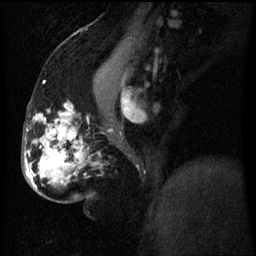
Breast MRI (dynamic contrast-enhanced), one sagittal slice; position 31 of 60 along the scan axis; dynamic contrast-enhanced series, image 2 of 3 at this slice position (ordered by acquisition); 1.5 T; TE 4.2 ms, TR 8 ms; 2.5 mm slice thickness; 256 × 256 image matrix, field of view 200 × 200 mm. Patient: female, 50 years.
Annotated regions visible in this slice (semi-automatically segmented with operator editing):
- analysis volume of interest (the breast-tissue region the enhancement analysis was run in; not a lesion): bounding box (x1, y1, x2, y2) in pixels: (26, 128, 83, 187)
- tumour enhancement mask (voxels above the 70 % enhancement threshold inside the analysis volume of interest): (28, 132, 63, 181)